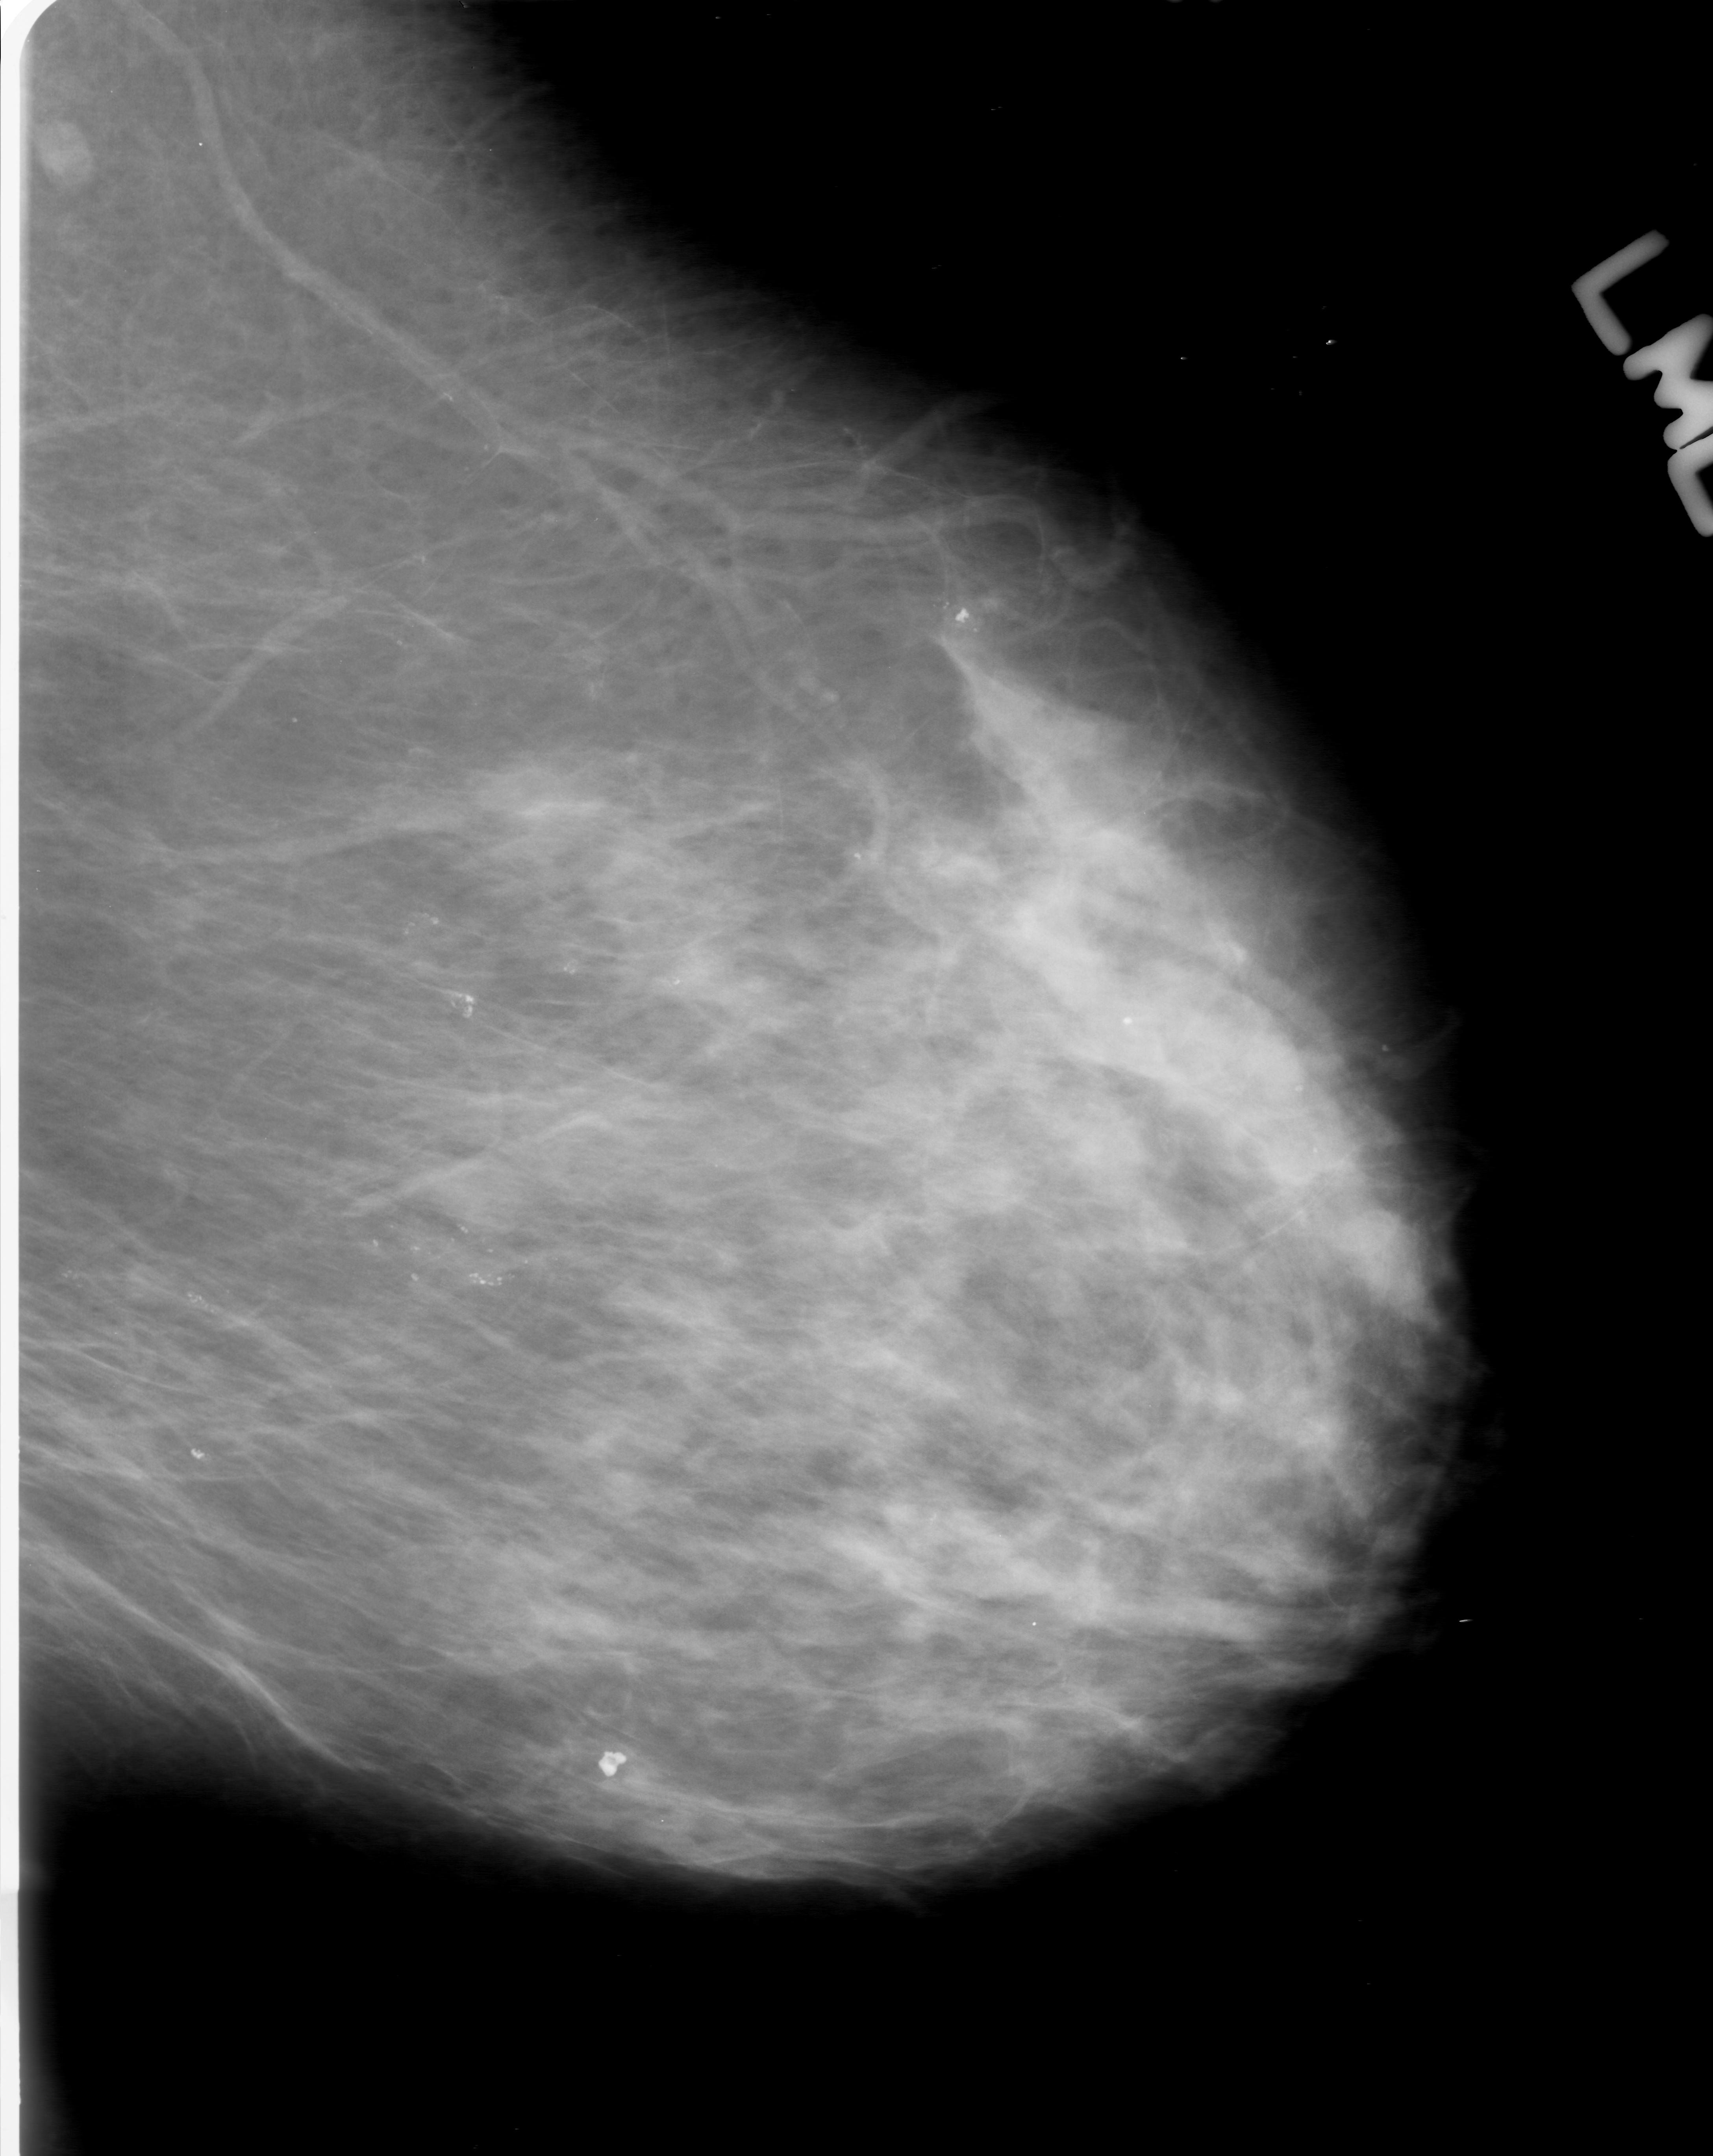
Digitized screen-film mammogram; left breast; MLO view; breast composition: scattered fibroglandular densities (BI-RADS density category 2 of 4).
- Marked findings (only marked abnormalities are described; nothing is implied about the rest of the image): calcifications, morphology round and regular / pleomorphic, distribution clustered; BI-RADS assessment category 0 (incomplete: needs additional imaging); subtlety rating 4 on a 1 (subtle) to 5 (obvious) scale; pathology (as recorded): benign.